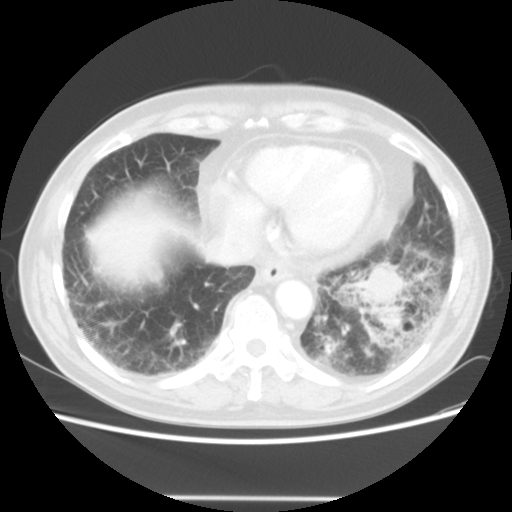
Chest CT, one axial slice. Position 13 of 56 along the scan axis. Lung window (W 1500 / L -600 HU). 5 mm slice thickness. 512 × 512 image matrix, field of view 360 × 360 mm. Male patient, age 66 years. Case-level facts recorded for this patient, not image findings: clinical TNM (as recorded): T4 N3 M0; histopathological grade: G3.
Outlined on this slice (rectangle marked by the reading radiologist):
- lung tumour (recorded histology: small cell carcinoma): box from (x=349, y=254) to (x=406, y=347) px